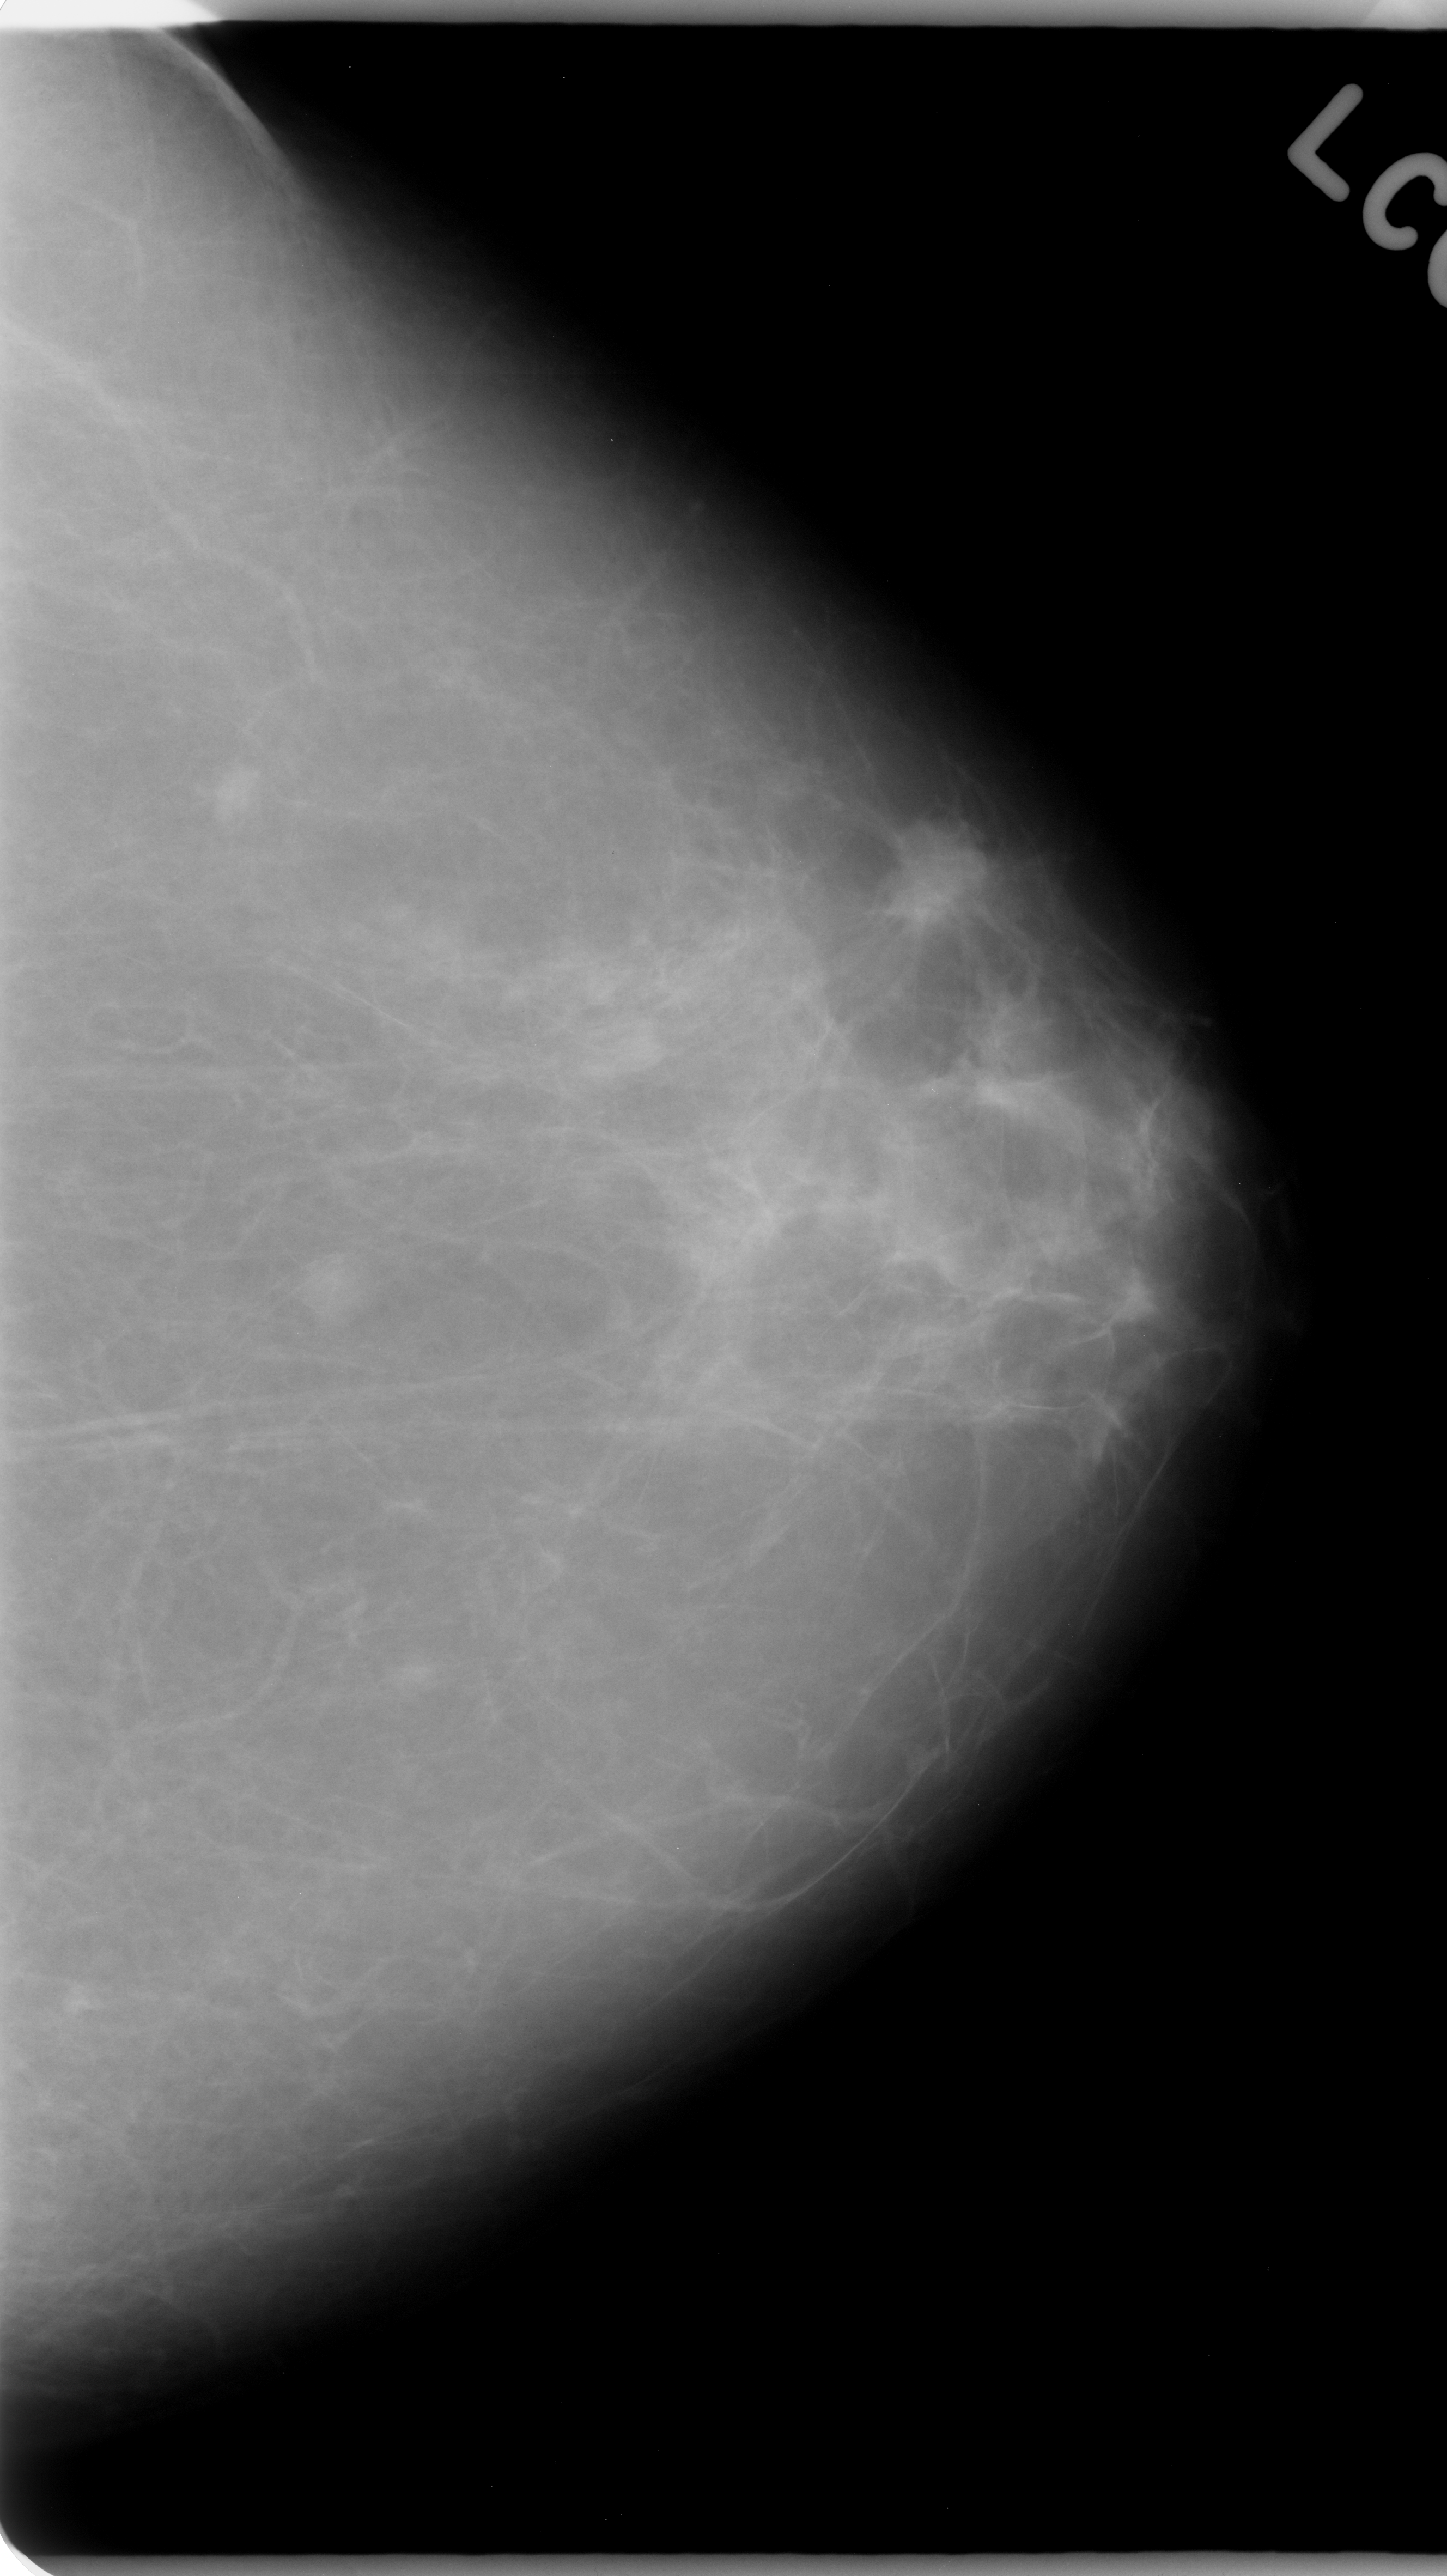
Digitized screen-film mammogram; left breast; CC view.
Marked findings (only marked abnormalities are described; nothing is implied about the rest of the image): mass, shape irregular, margins spiculated; BI-RADS assessment category 5; subtlety rating 5 on a 1 (subtle) to 5 (obvious) scale; pathology result (as recorded, not read from the image): malignant.